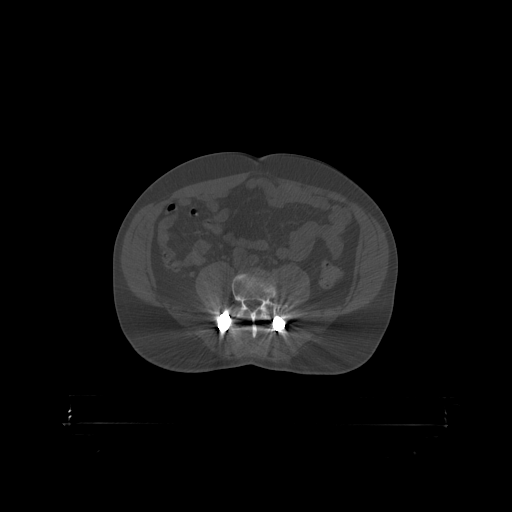
CT including the spine, one axial slice. Slice 216 of 399 in the series (ordered by position). Bone window (W 1800 / L 400 HU). 1.25 mm slice thickness. 512 × 512 image matrix. Patient: male, 46 years. Case-level facts recorded for this patient, not image findings: primary cancer: skin.
Annotated regions visible in this slice (semi-automatic segmentation, software-assisted and operator-edited):
- L4 vertebra: bounding box <235,312,271,319> (left, top, right, bottom; pixels)
- L5 vertebra: <218,274,290,319>